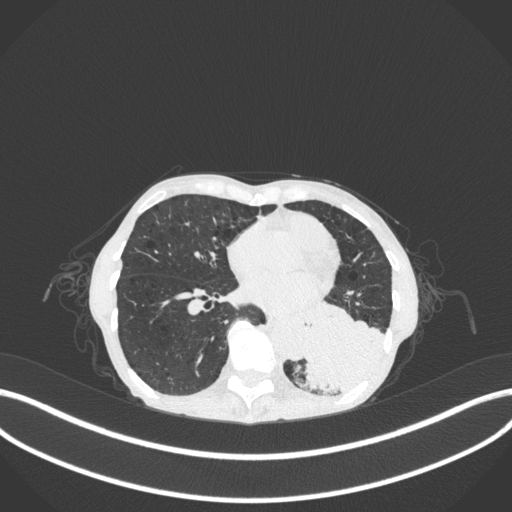
Chest CT, one axial slice. Position 105 of 347 along the scan axis. Reconstruction kernel B31f. 120 kVp. Lung window (W 1500 / L -600 HU). 512 × 512 image matrix, field of view 400 × 400 mm. Patient: female, 70 years. Case-level facts recorded for this patient, not image findings: clinical TNM (as recorded): T3 N0 M0.
Outlined on this slice (bounding box drawn by a radiologist):
- lung tumour (recorded histology: small cell carcinoma): bounding box (x1, y1, x2, y2) in pixels: (295, 288, 391, 395)